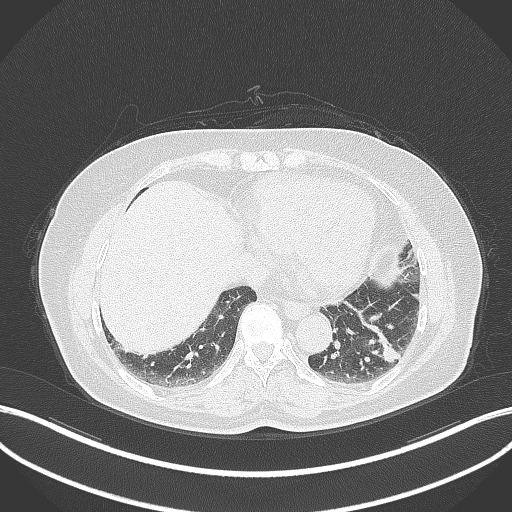
Chest CT, one axial slice. Position 116 of 311 along the scan axis. Reconstruction kernel B70f. 120 kVp. Lung window (W 1500 / L -600 HU). 1 mm slice thickness. 512 × 512 image matrix, field of view 400 × 400 mm. Female patient, age 59 years. From the clinical record (not read from this slice): clinical TNM (as recorded): T2a N0 M0; histopathological grade: G2-3.
Structures marked on this image (rectangle marked by the reading radiologist):
- lung tumour (recorded histology: adenocarcinoma): bounding box (x1, y1, x2, y2) in pixels: (367, 324, 402, 363)